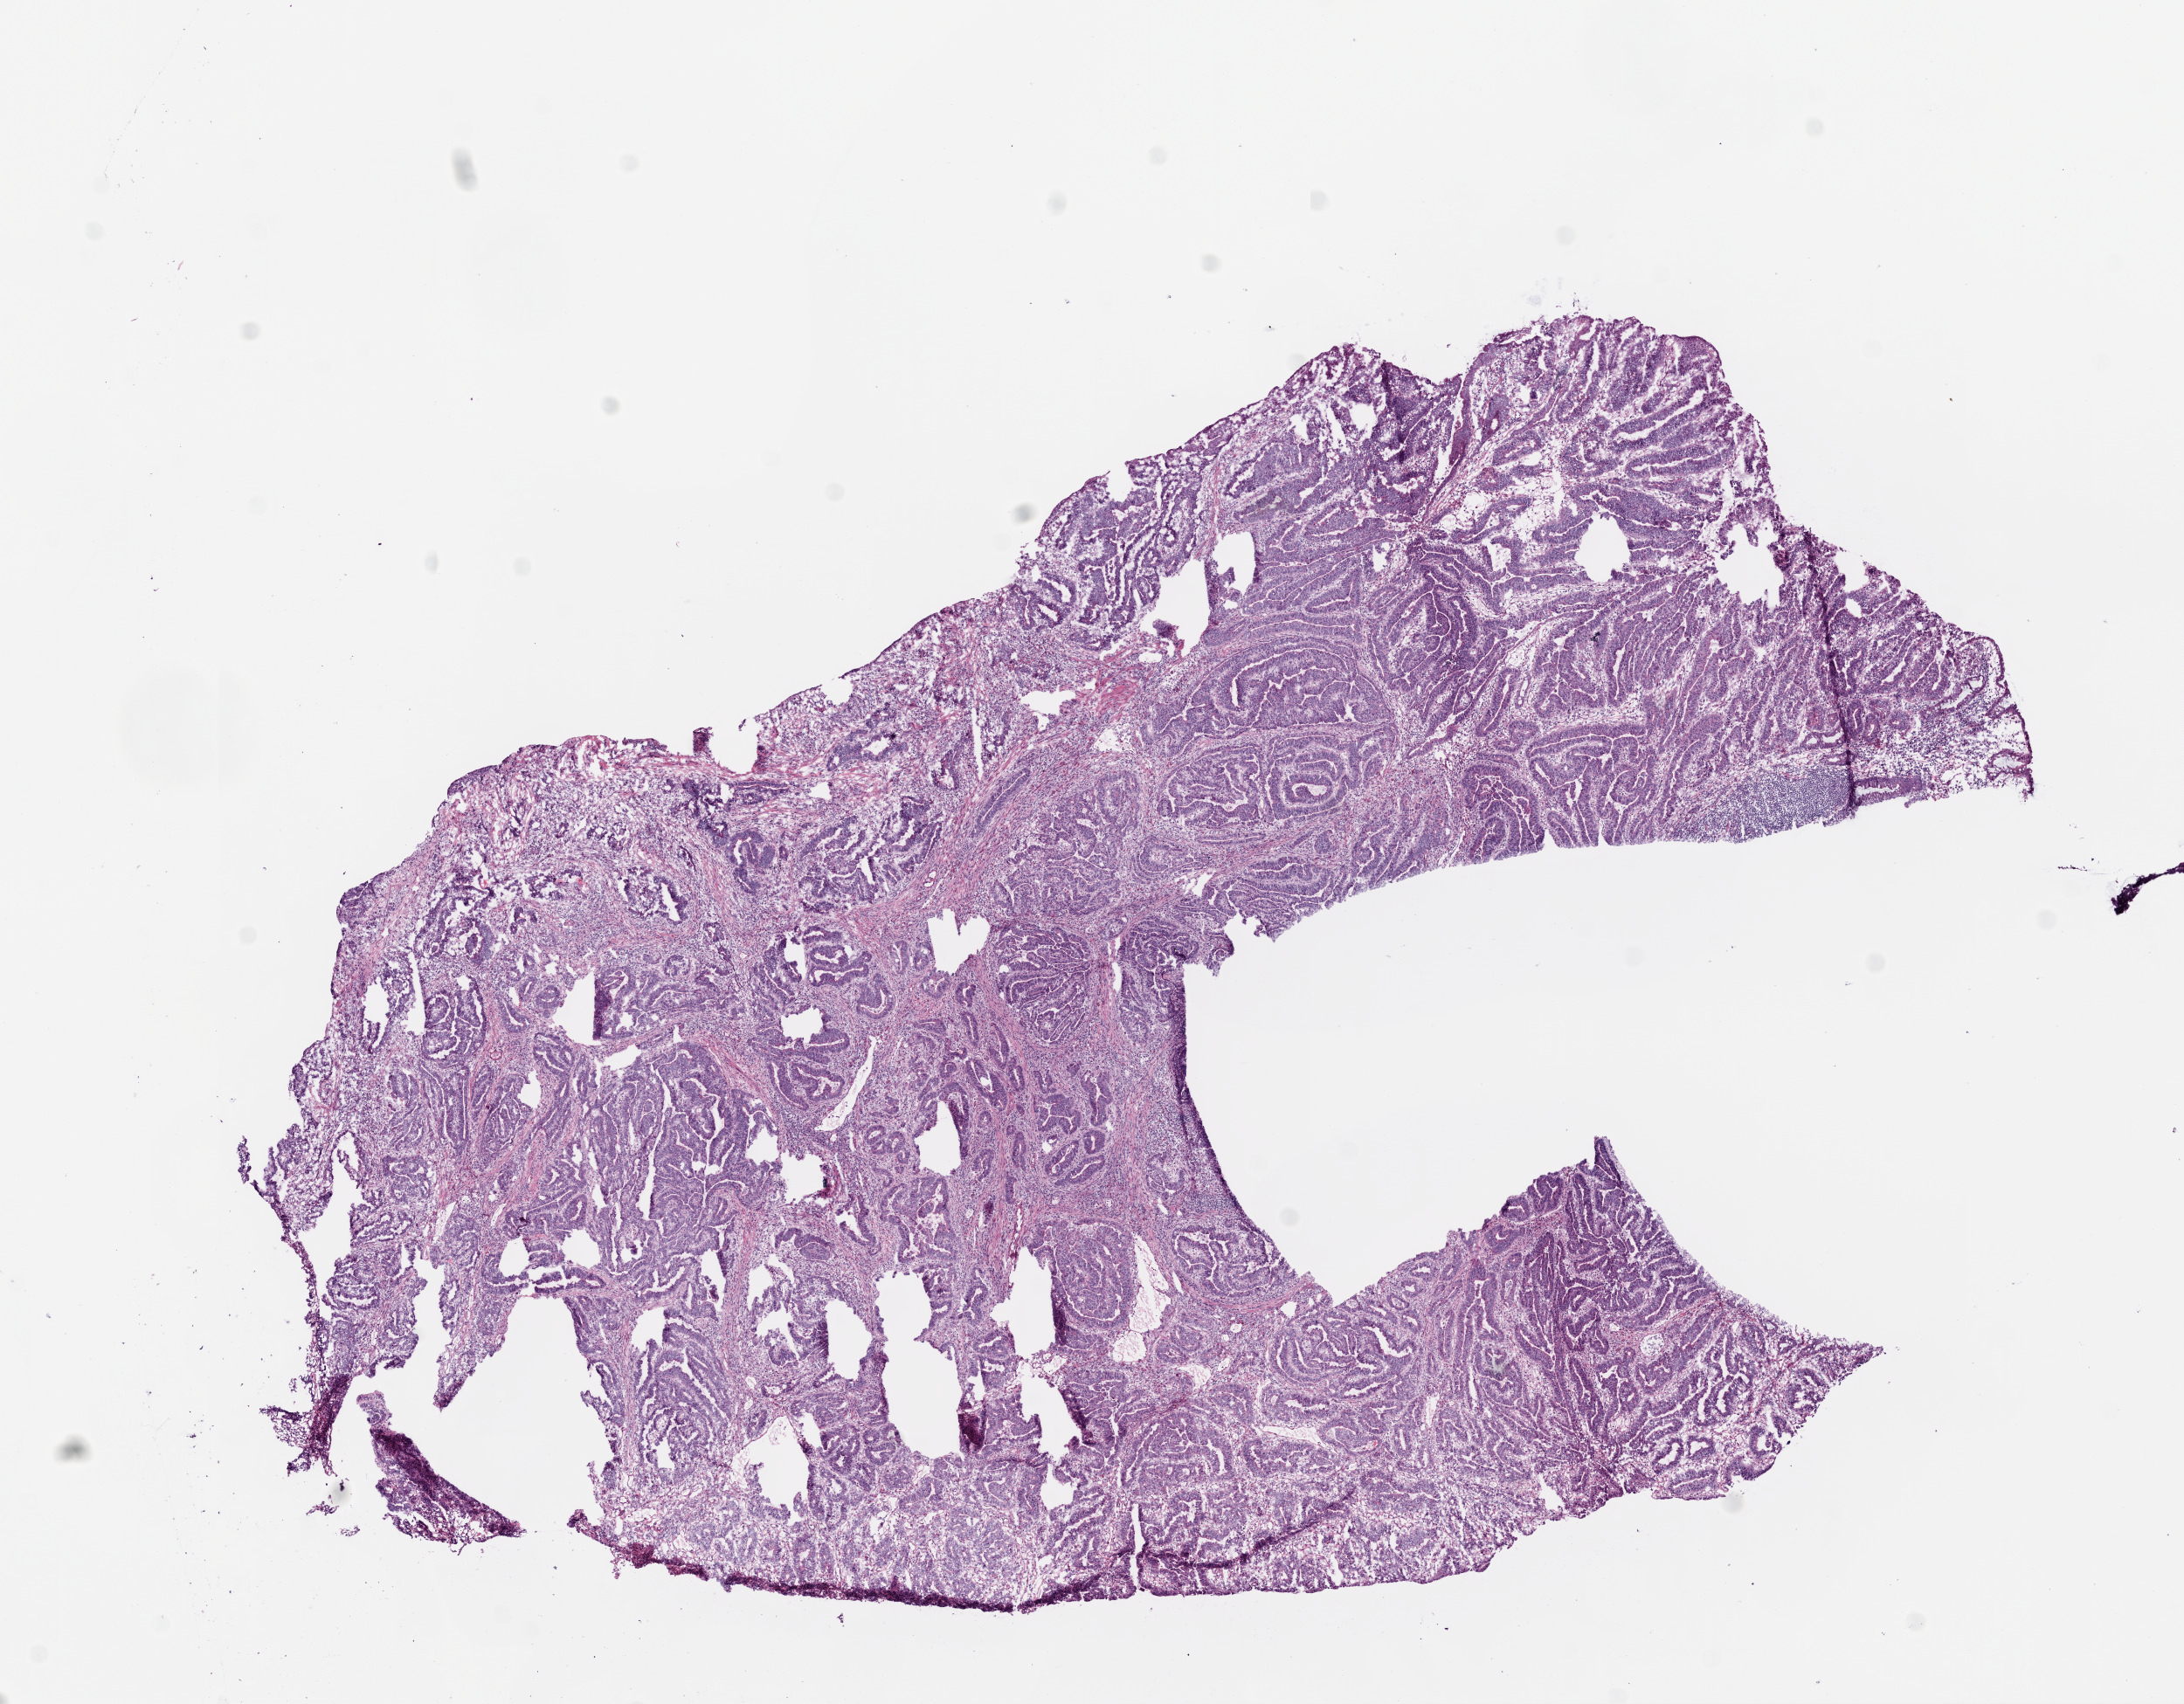
Whole-slide histology image, Hematoxylin and eosin (H&E) stained — whole scanned area (about 10.0 x 7.8 mm) shown as a low-resolution overview. Frozen section. Sample: primary tumour, colon. Male, age 68 years at initial diagnosis. Pathologist review of this section (percent, as recorded): tumour cells 60%, tumour nuclei 80%, normal cells 0%, stromal cells 40%, necrosis 0%.
AJCC pathologic stage: I (6th edition). Histologic diagnosis: Adenocarcinoma, NOS. Lymph nodes positive (case pathology): 0 of 21 examined.